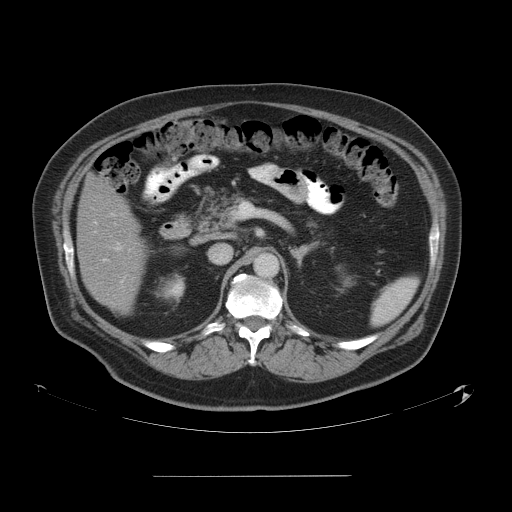
Contrast-enhanced abdominal CT, one axial slice; position 27 of 58 along the scan axis; 120 kVp; intravenous contrast given; soft-tissue window (W 400 / L 40 HU); 5 mm slice thickness; 512 × 512 image matrix, field of view 480 × 480 mm. Male patient, age 63 years. Case-level facts recorded for this patient, not image findings: diagnosis: colorectal cancer liver metastases, imaged before liver resection; multiple liver metastases: no; largest metastasis: 4.2 cm; disease in both lobes: no.
Annotated regions visible in this slice (expert manual segmentation):
- hepatic veins: bounding box <121,280,124,282> (left, top, right, bottom; pixels)
- liver: <77,178,143,311>
- planned liver remnant (the part of the liver to remain after resection): <77,178,143,311>
- portal vein (with intrahepatic branches): <95,222,120,261>